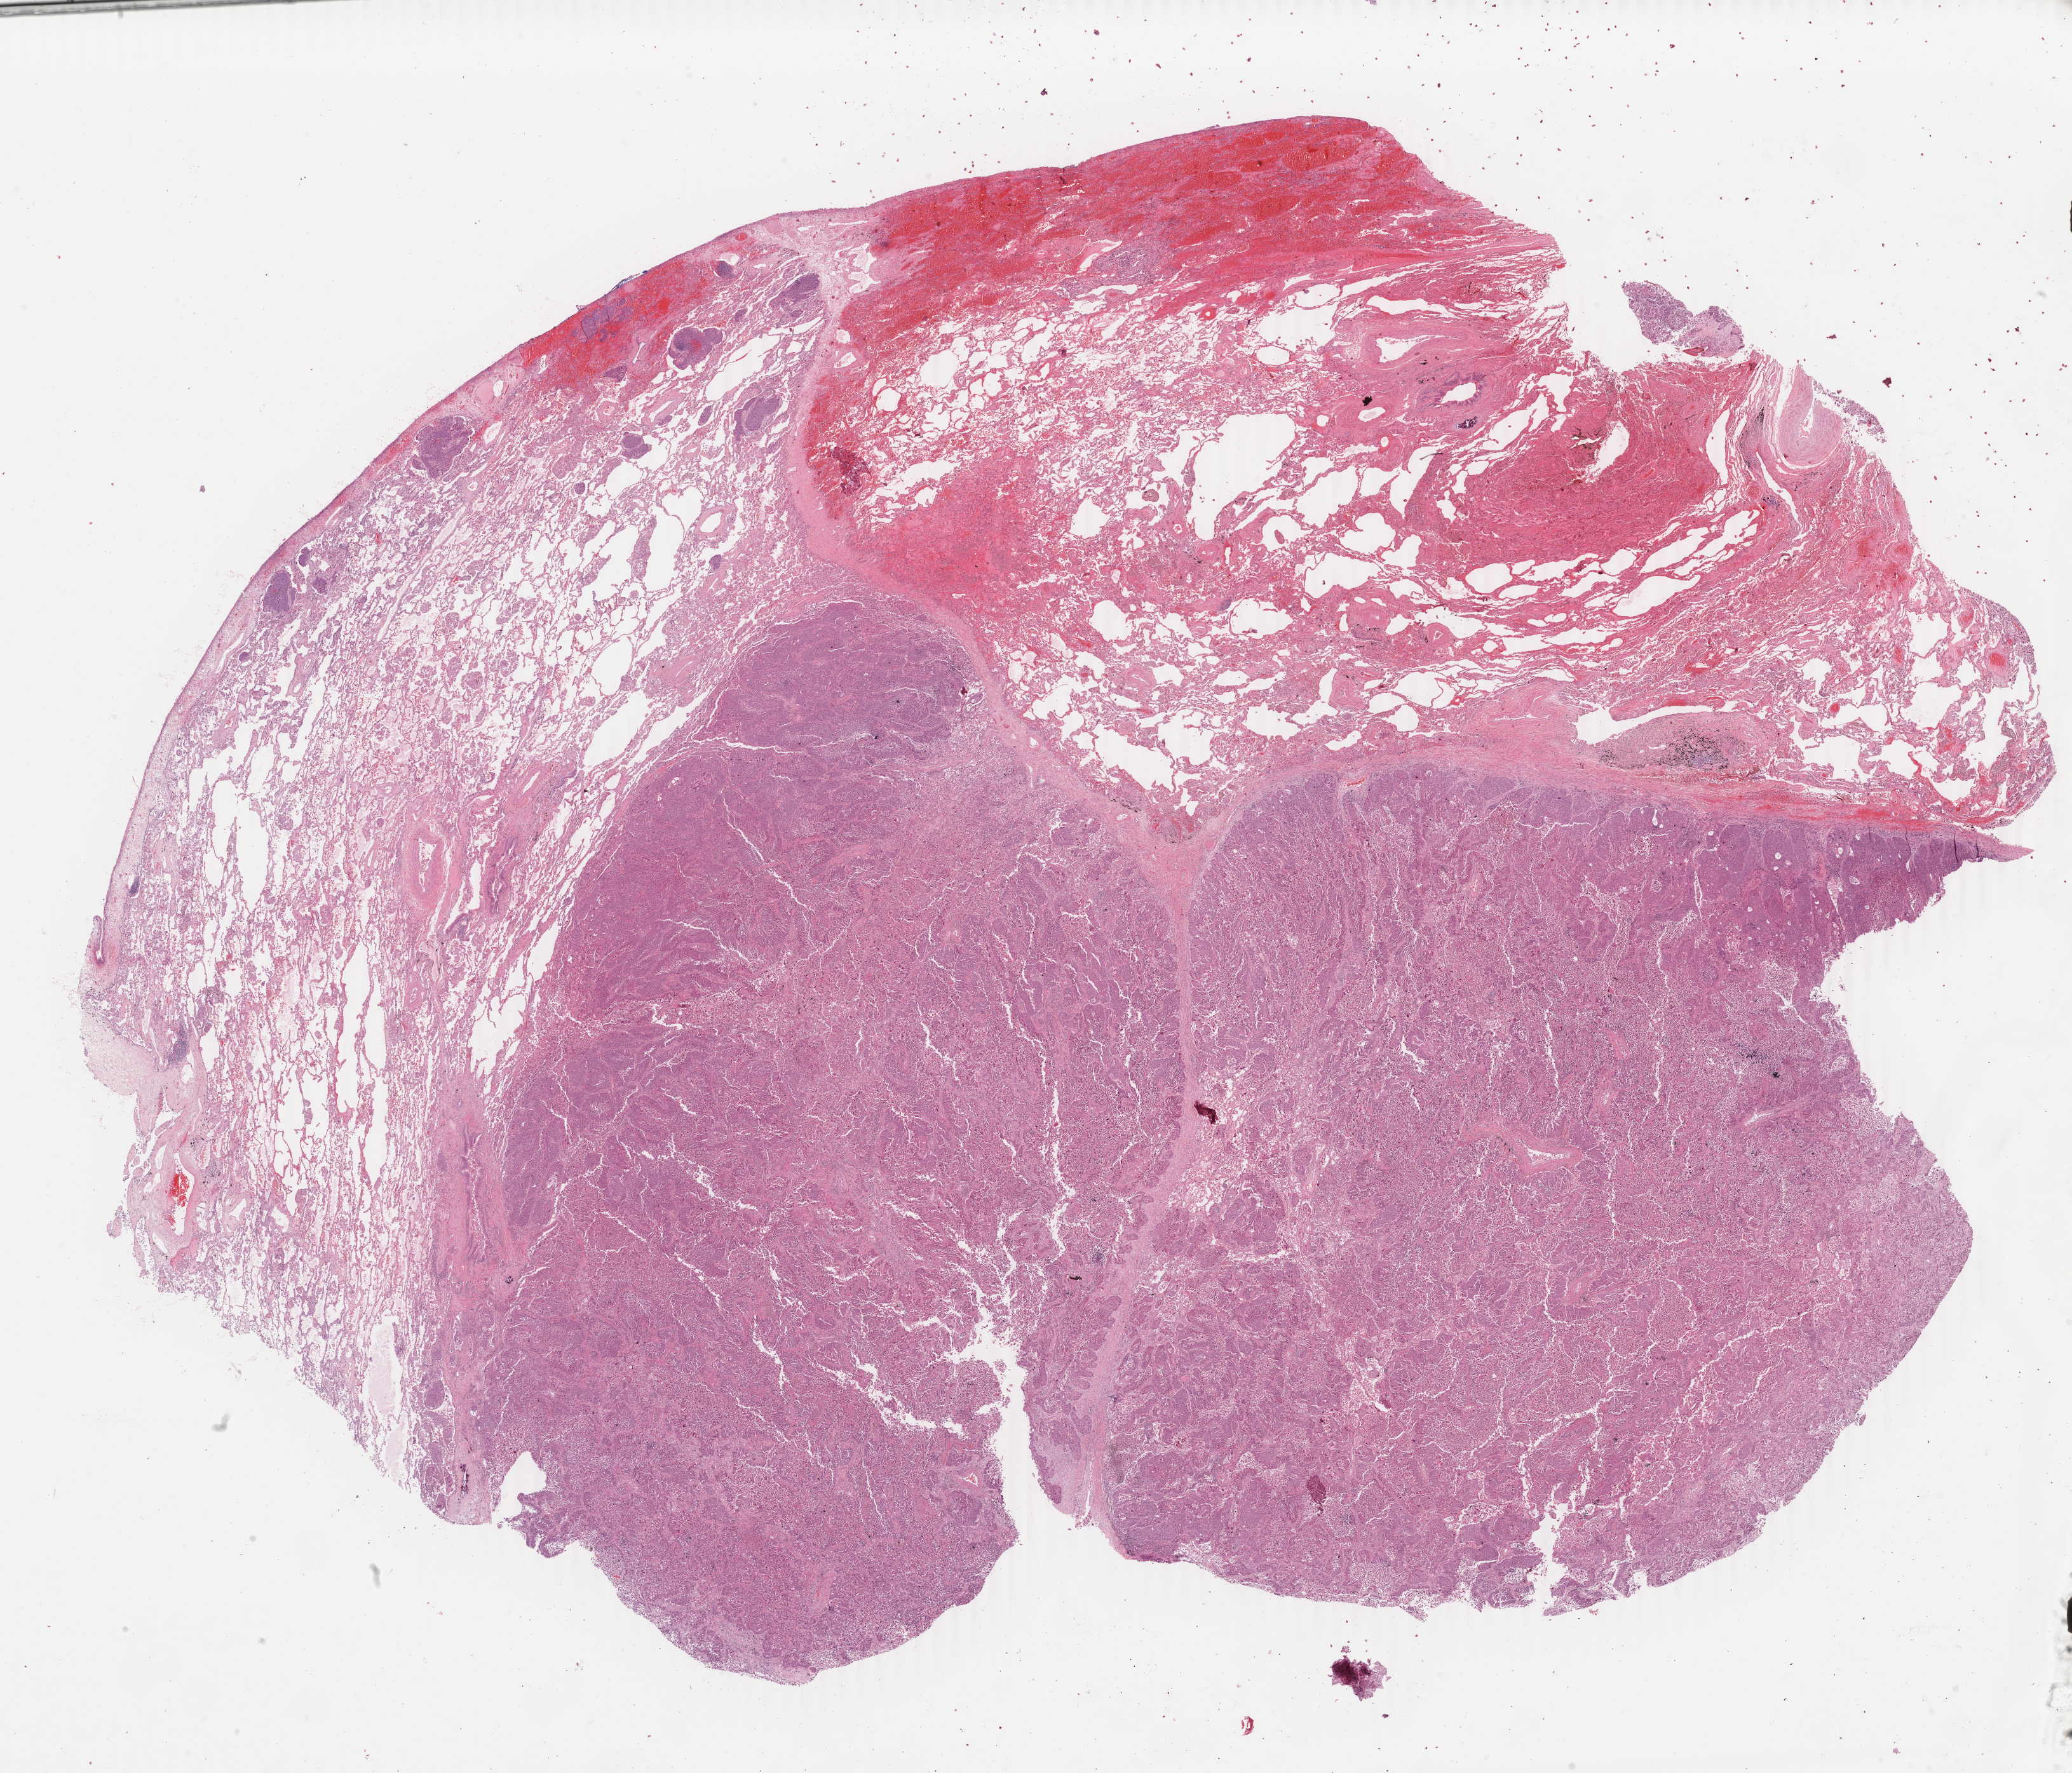
H&E whole-slide image — whole scanned area (about 25.9 x 22.2 mm, from a 40x scan) shown as a low-resolution overview. Formalin-fixed paraffin-embedded (FFPE) diagnostic section. Sample: primary tumour, lung. Male, age 67 years at initial diagnosis.
Pathologic diagnosis: Squamous cell carcinoma, NOS (upper lobe, lung). AJCC pathologic stage: IV (7th edition). TNM: T4 N0 M1a. Laterality: left.